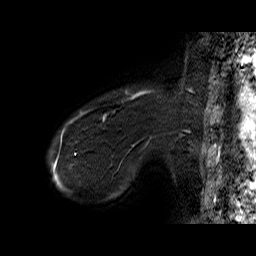
Breast MRI (dynamic contrast-enhanced), one sagittal slice. Position 7 of 60 along the scan axis. Dynamic contrast-enhanced series, time point 2 of 6 at this slice position (early post-contrast). 1.5 T. TE 6.4 ms, TR 32.9 ms. 4 mm slice thickness. 256 × 256 image matrix, field of view 200 × 200 mm. Female patient. From the clinical record (not read from this slice): setting: breast cancer imaged before/during neoadjuvant chemotherapy; receptor status: HER2-positive.
Structures marked on this image (semi-automatically segmented with operator editing):
- analysis volume of interest (the breast-tissue region the enhancement analysis was run in; not a lesion): bounding box [x1, y1, x2, y2] px = [71, 86, 155, 146]
- tumour enhancement mask (voxels above the 100 % enhancement threshold inside the analysis volume of interest): [71, 90, 152, 123]